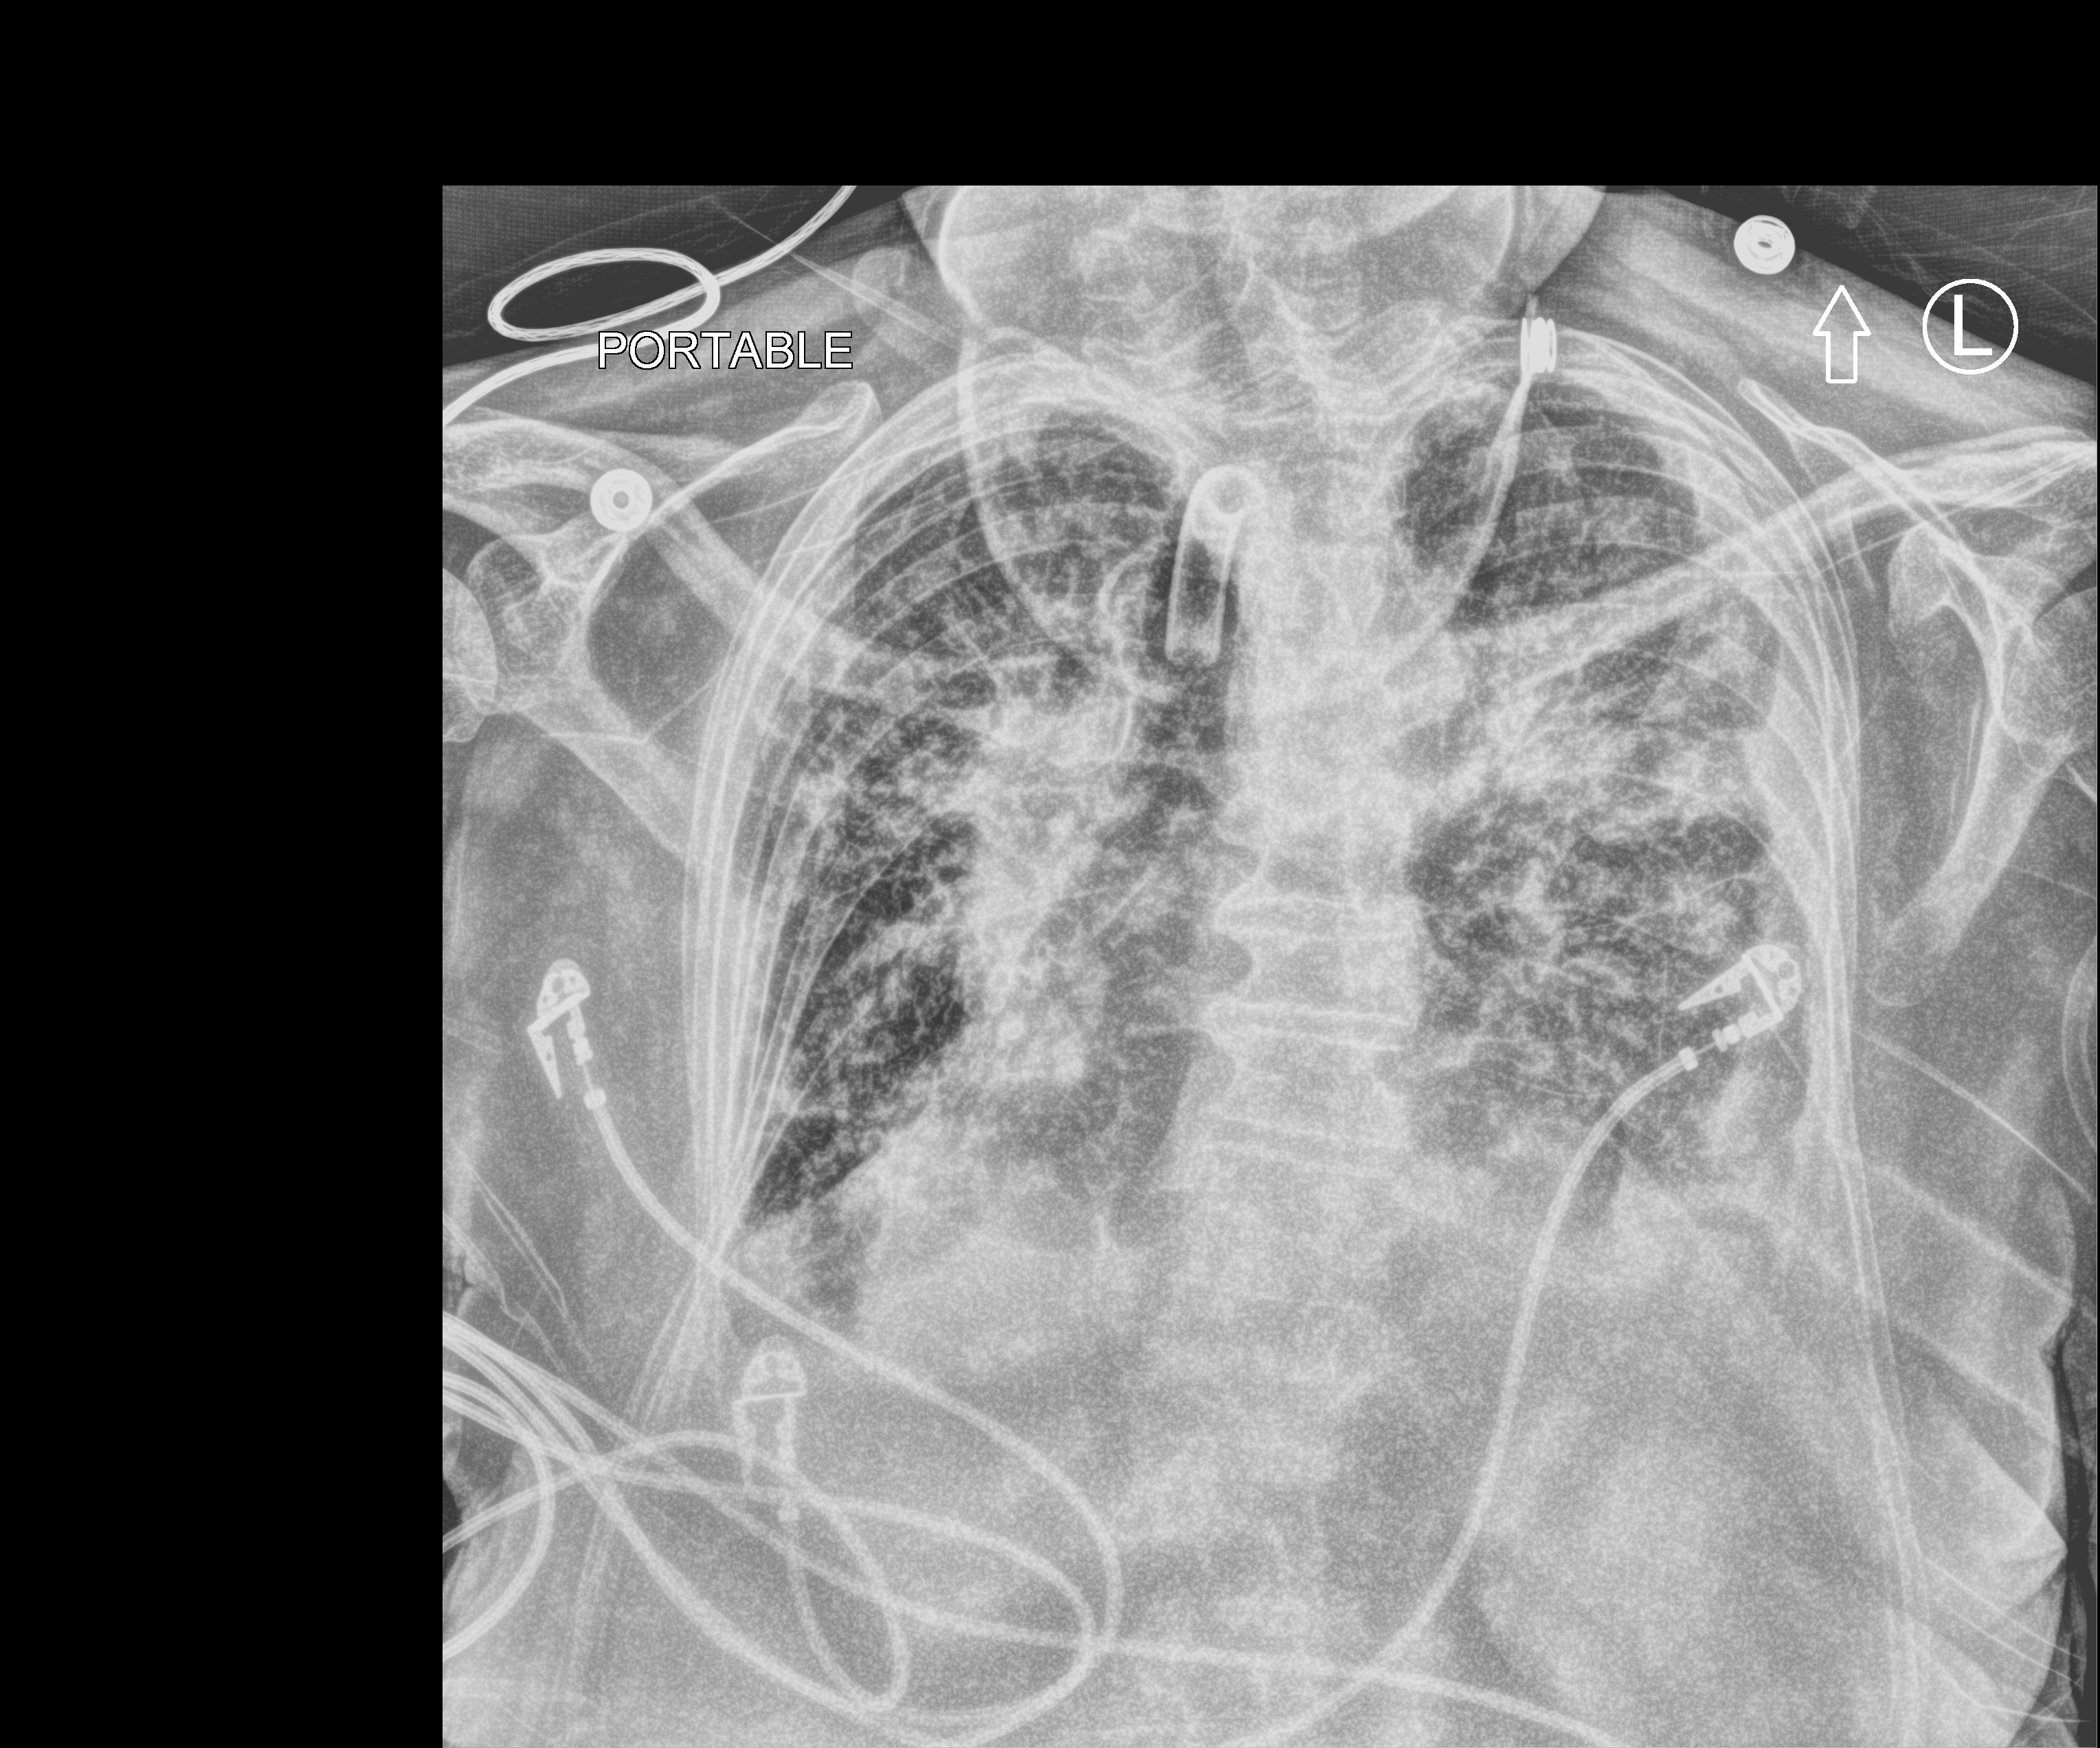
Portable chest radiograph, anteroposterior (AP) projection. Female patient hospitalised with COVID-19, age 75–90 years.
From the hospital-stay record, not from the radiograph (when in the stay this image was taken is not recorded):
- mechanically ventilated during this hospital stay: yes
- hypertension (admission record): yes
- admitted to intensive care during this hospital stay: yes